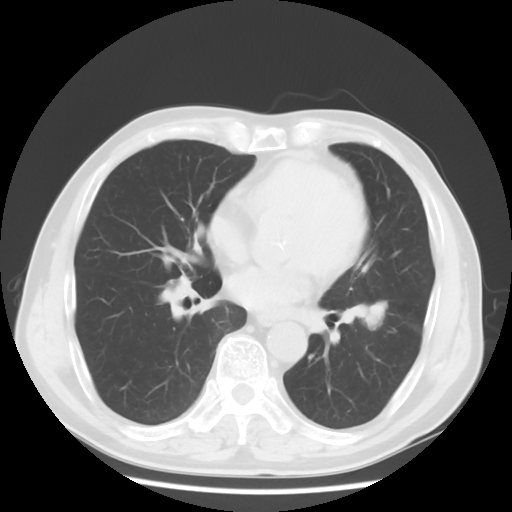
Chest CT, one axial slice; slice 30 of 68 in the series (ordered by position); reconstruction kernel STANDARD; lung window (W 1500 / L -600 HU); 512 × 512 image matrix, field of view 360 × 360 mm. Patient: male, 71 years. From the clinical record (not read from this slice): clinical TNM (as recorded): T1c N1 M0; histopathological grade: G2-3.
Outlined on this slice (bounding box drawn by a radiologist):
- lung tumour (recorded histology: adenocarcinoma): bounding box <354,292,397,342> (left, top, right, bottom; pixels)